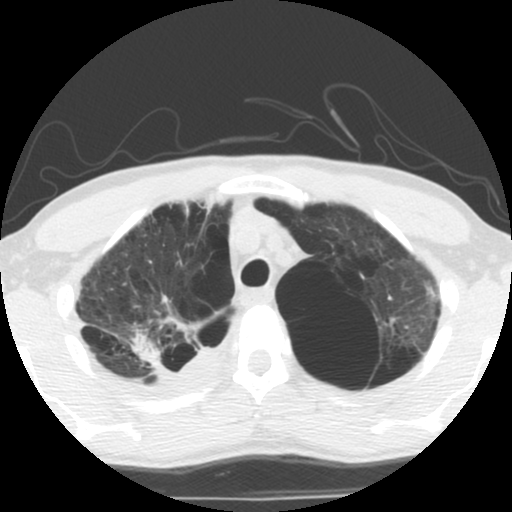
Low-dose screening chest CT, one axial slice. Position 94 of 119 along the scan axis. Reconstruction kernel STANDARD. Lung window (W 1500 / L -600 HU). 512 × 512 image matrix, field of view 295 × 295 mm.
Outlined on this slice (expert manual segmentation):
- lesion 1 (tumor, upper lobe of right lung): bounding box <133,328,163,361> (left, top, right, bottom; pixels)